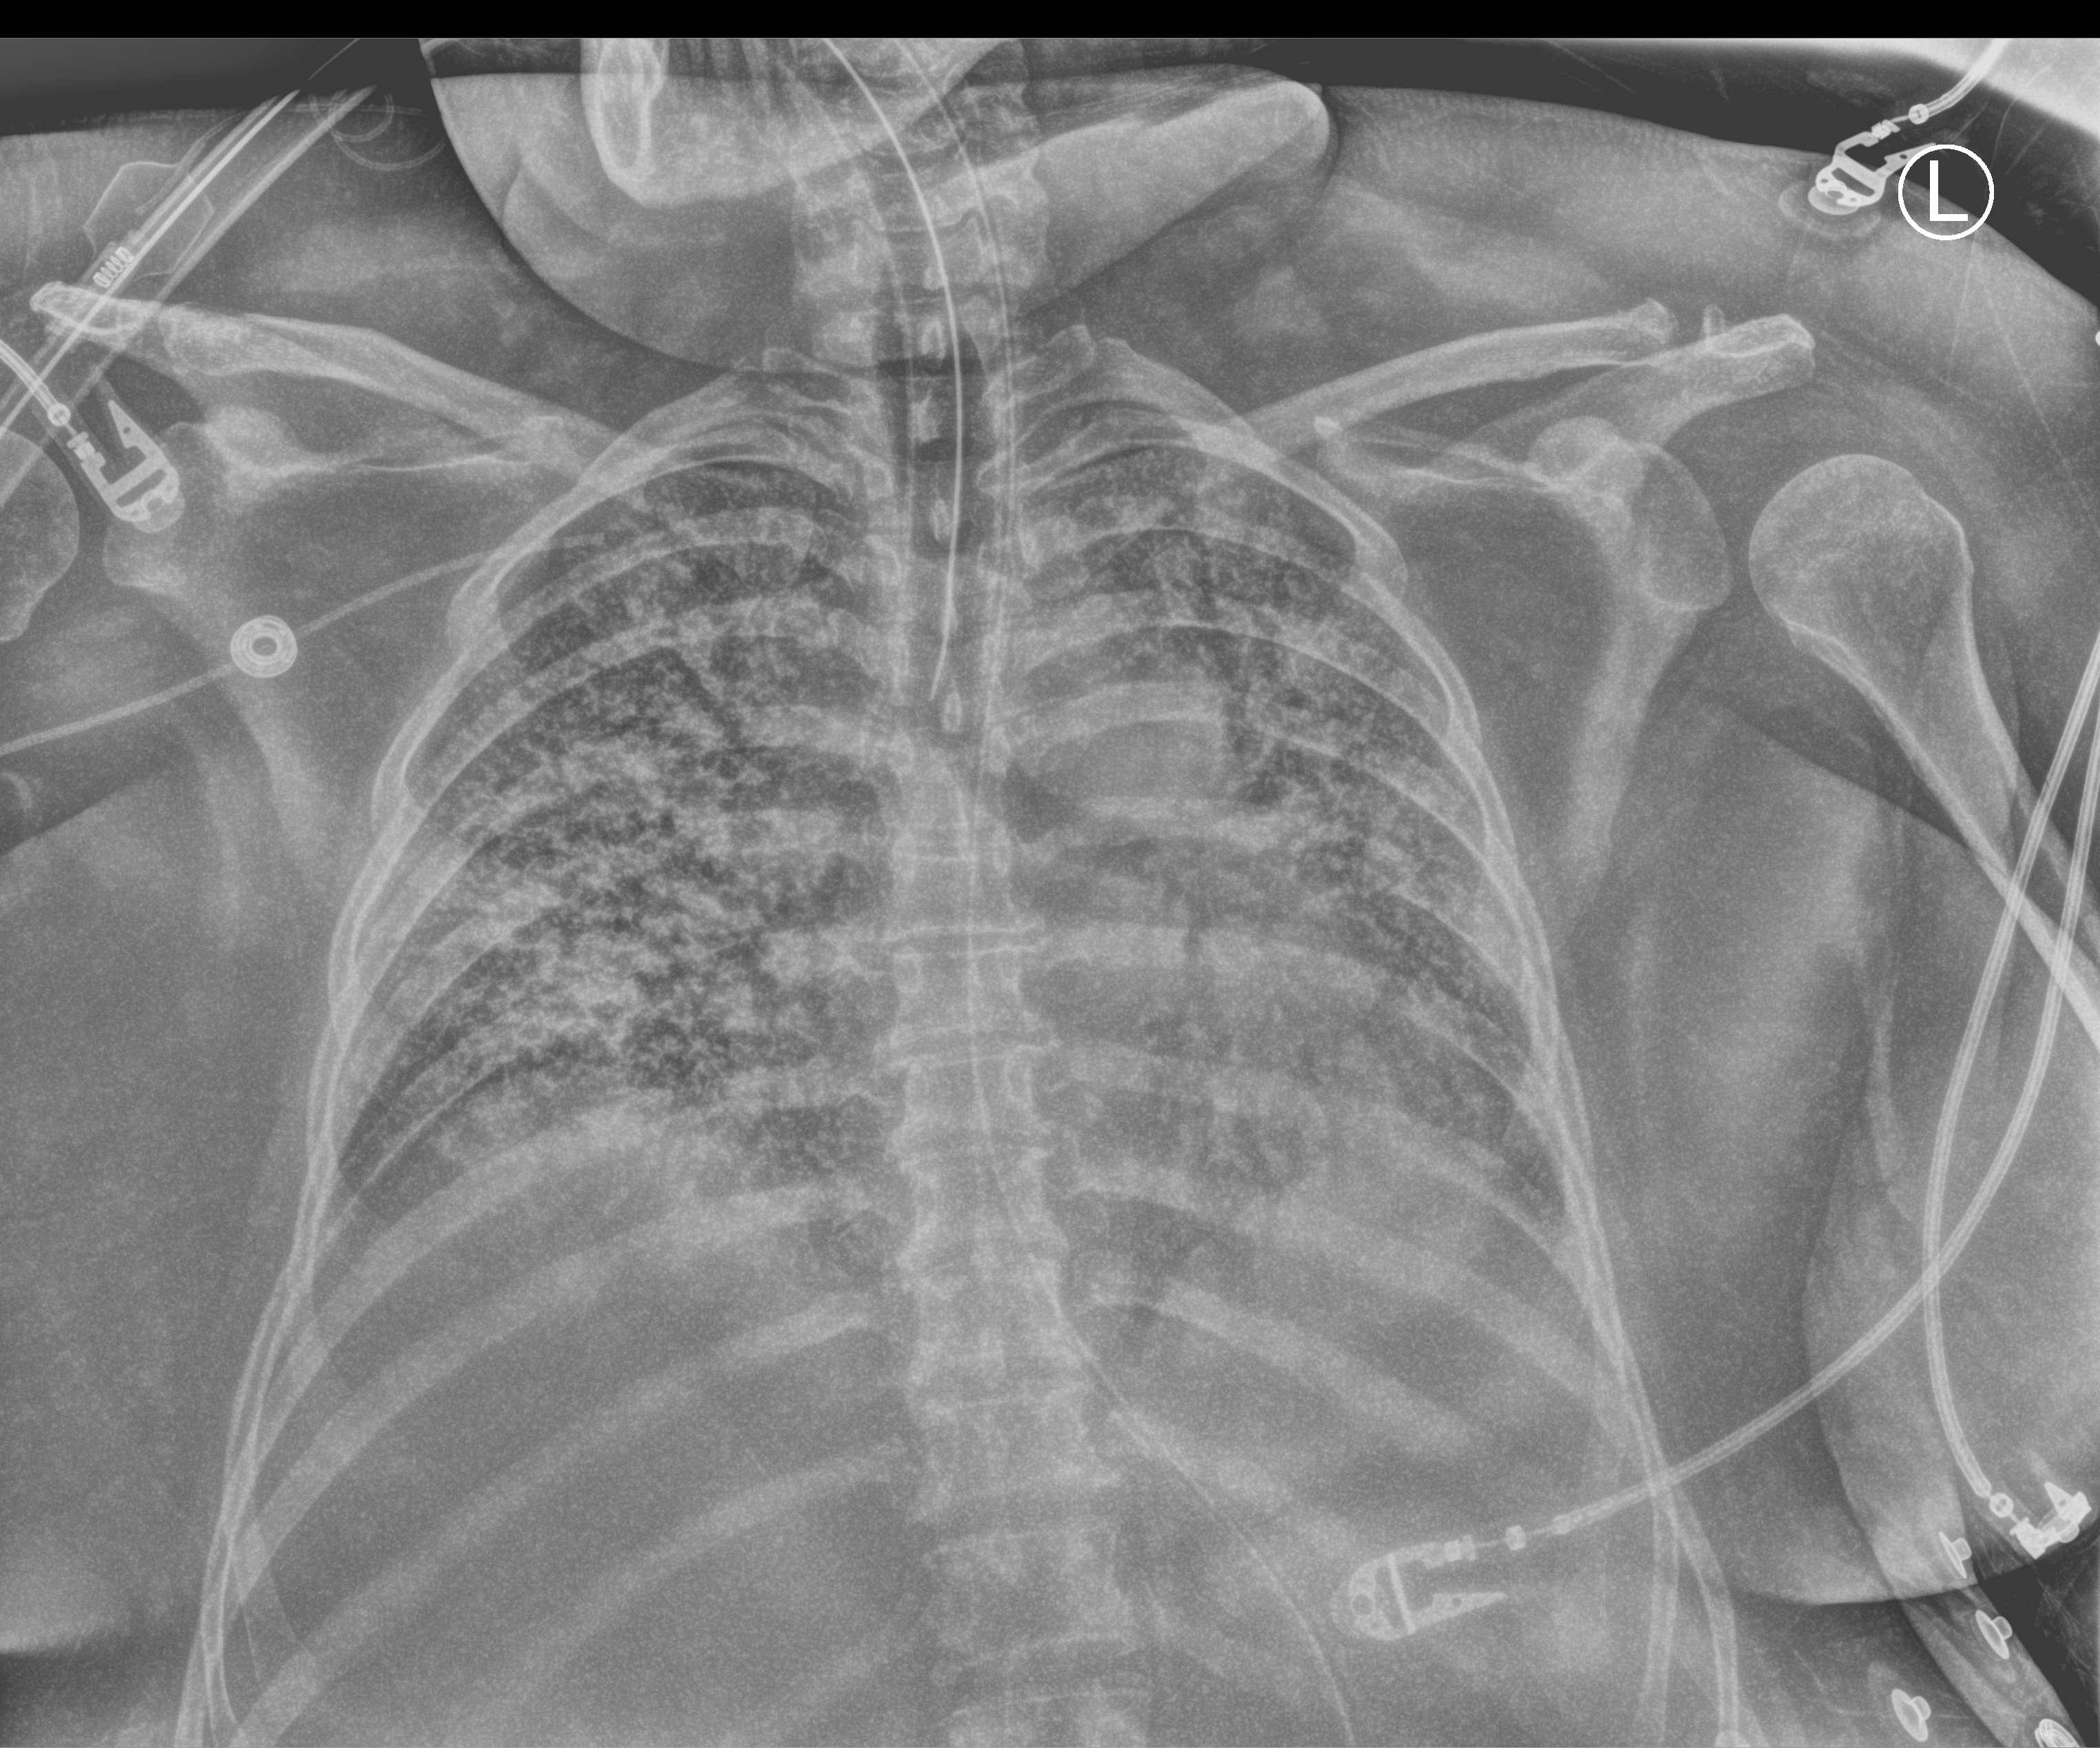
Bedside chest radiograph (computed radiography); anteroposterior (AP) projection. Female patient hospitalised with COVID-19, age 18–59 years.
From the hospital-stay record, not from the radiograph (when in the stay this image was taken is not recorded): admitted to intensive care during this hospital stay: yes.